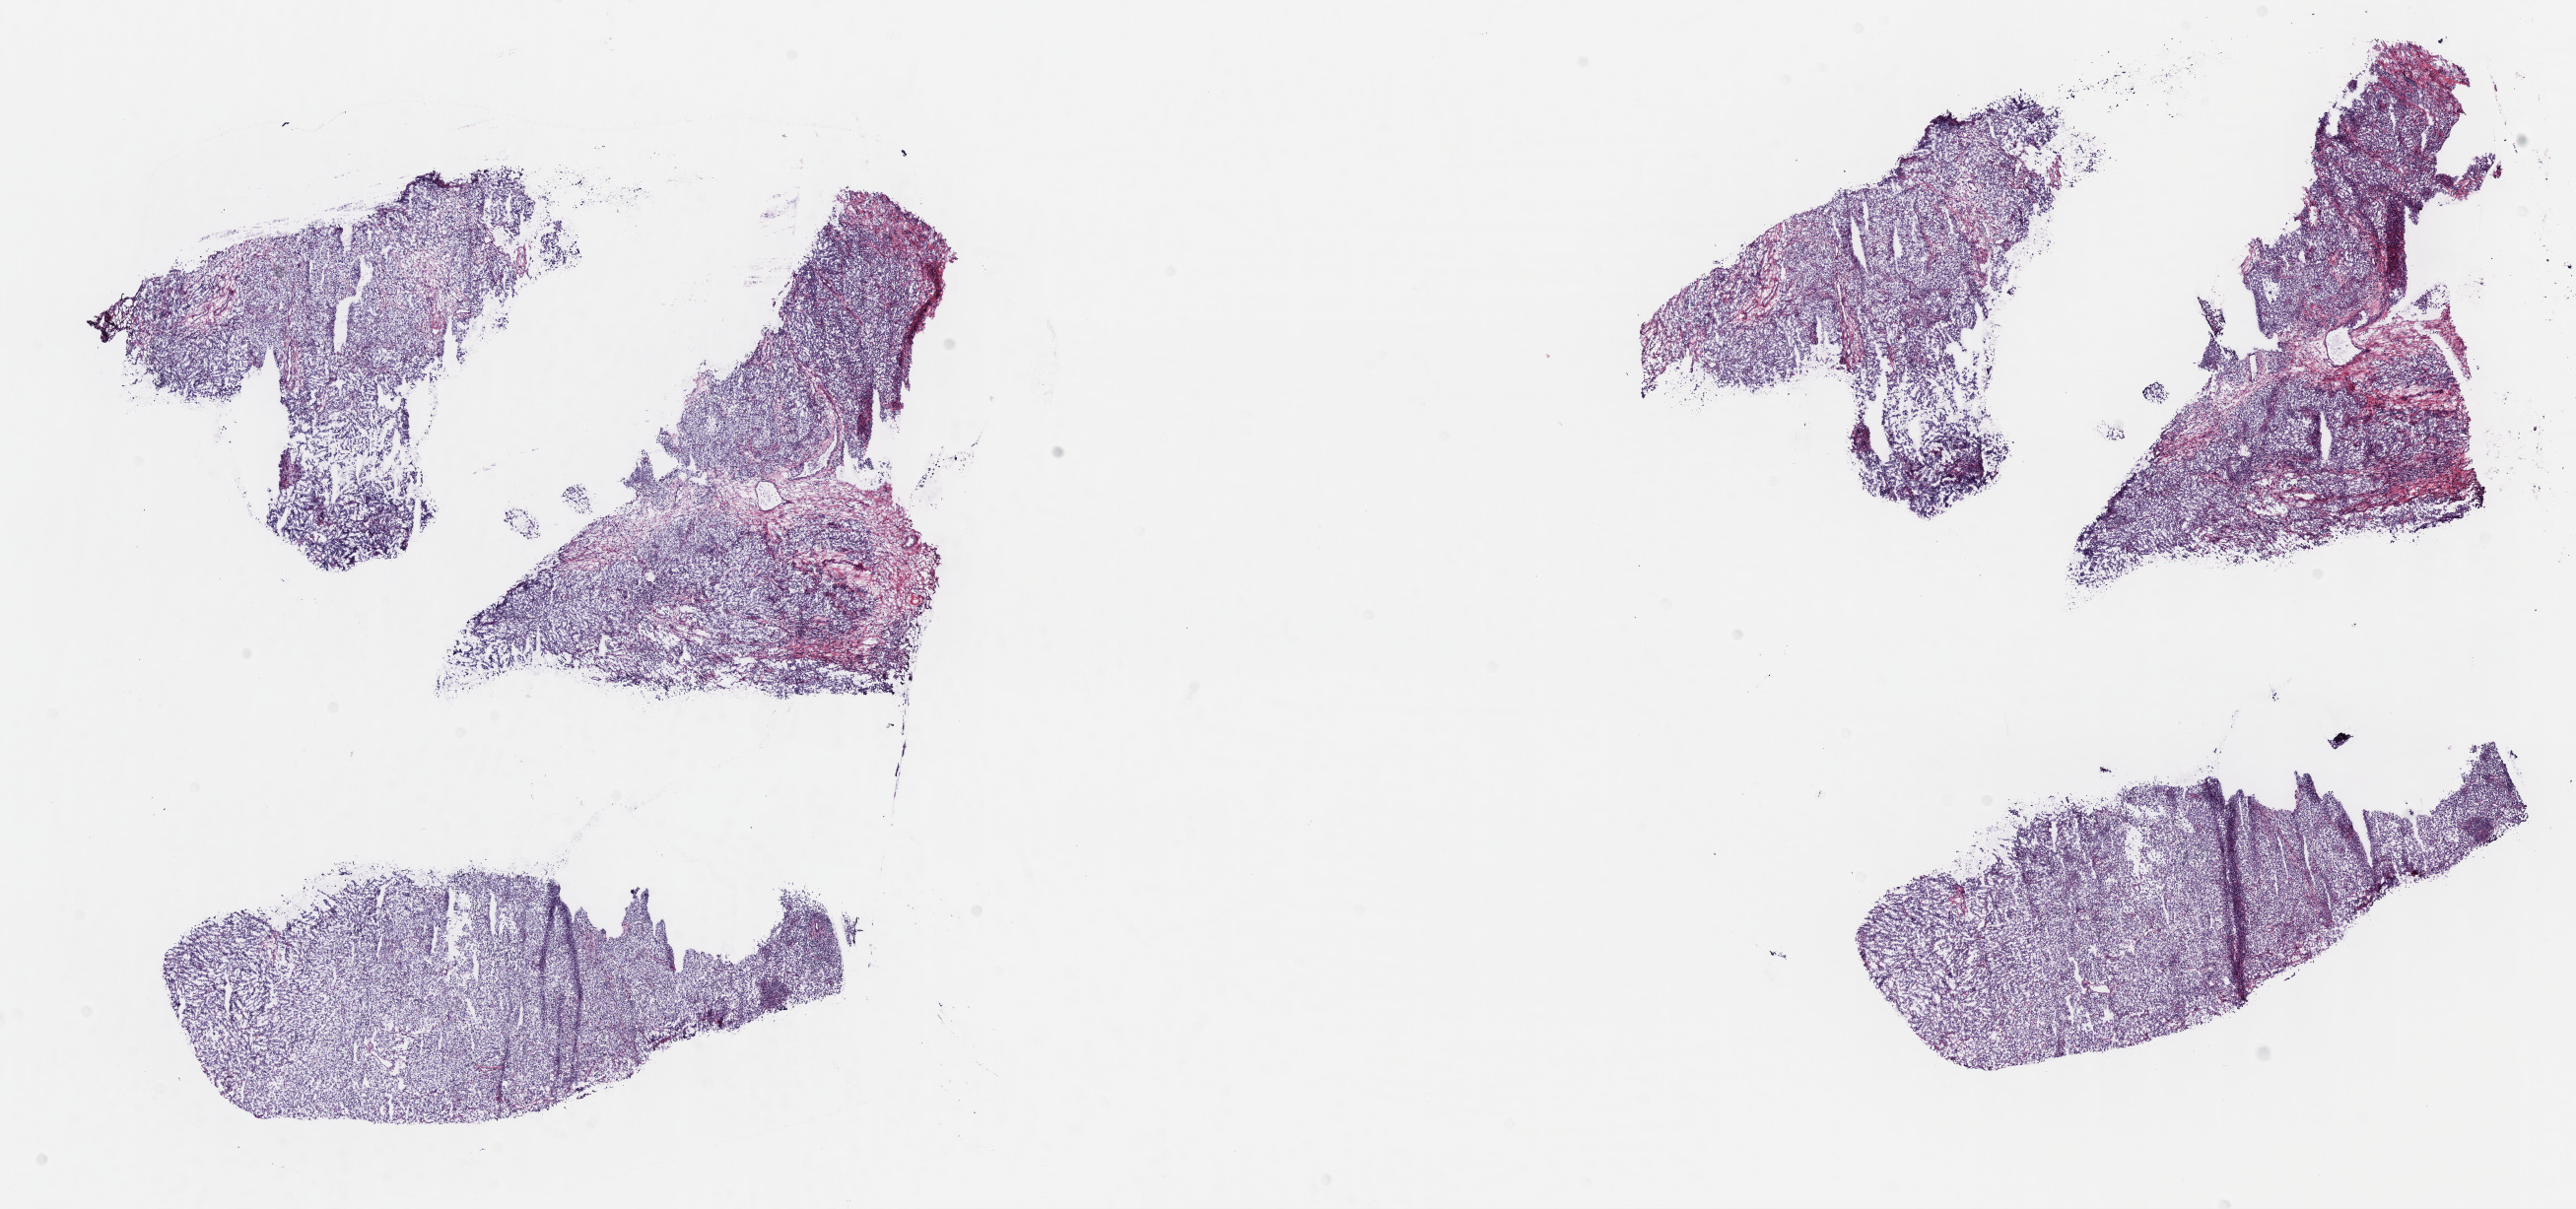
Whole-slide histology image, Hematoxylin and eosin (H&E) stained, low-resolution overview of the scanned area, about 21.1 x 9.9 mm (from a 40x scan); frozen section; primary tumour sample from the testis. Male, age 28 years at initial diagnosis. Composition of this section per pathologist review: tumour cells 85%, tumour nuclei 85%, normal cells 0%, stromal cells 15%, necrosis 0%. Inflammatory infiltration, as recorded: lymphocyte infiltration 60%, monocyte infiltration 20%, neutrophil infiltration 10%.
Laterality: right. Pathologic diagnosis: Seminoma, NOS. AJCC pathologic stage: IS (7th edition).